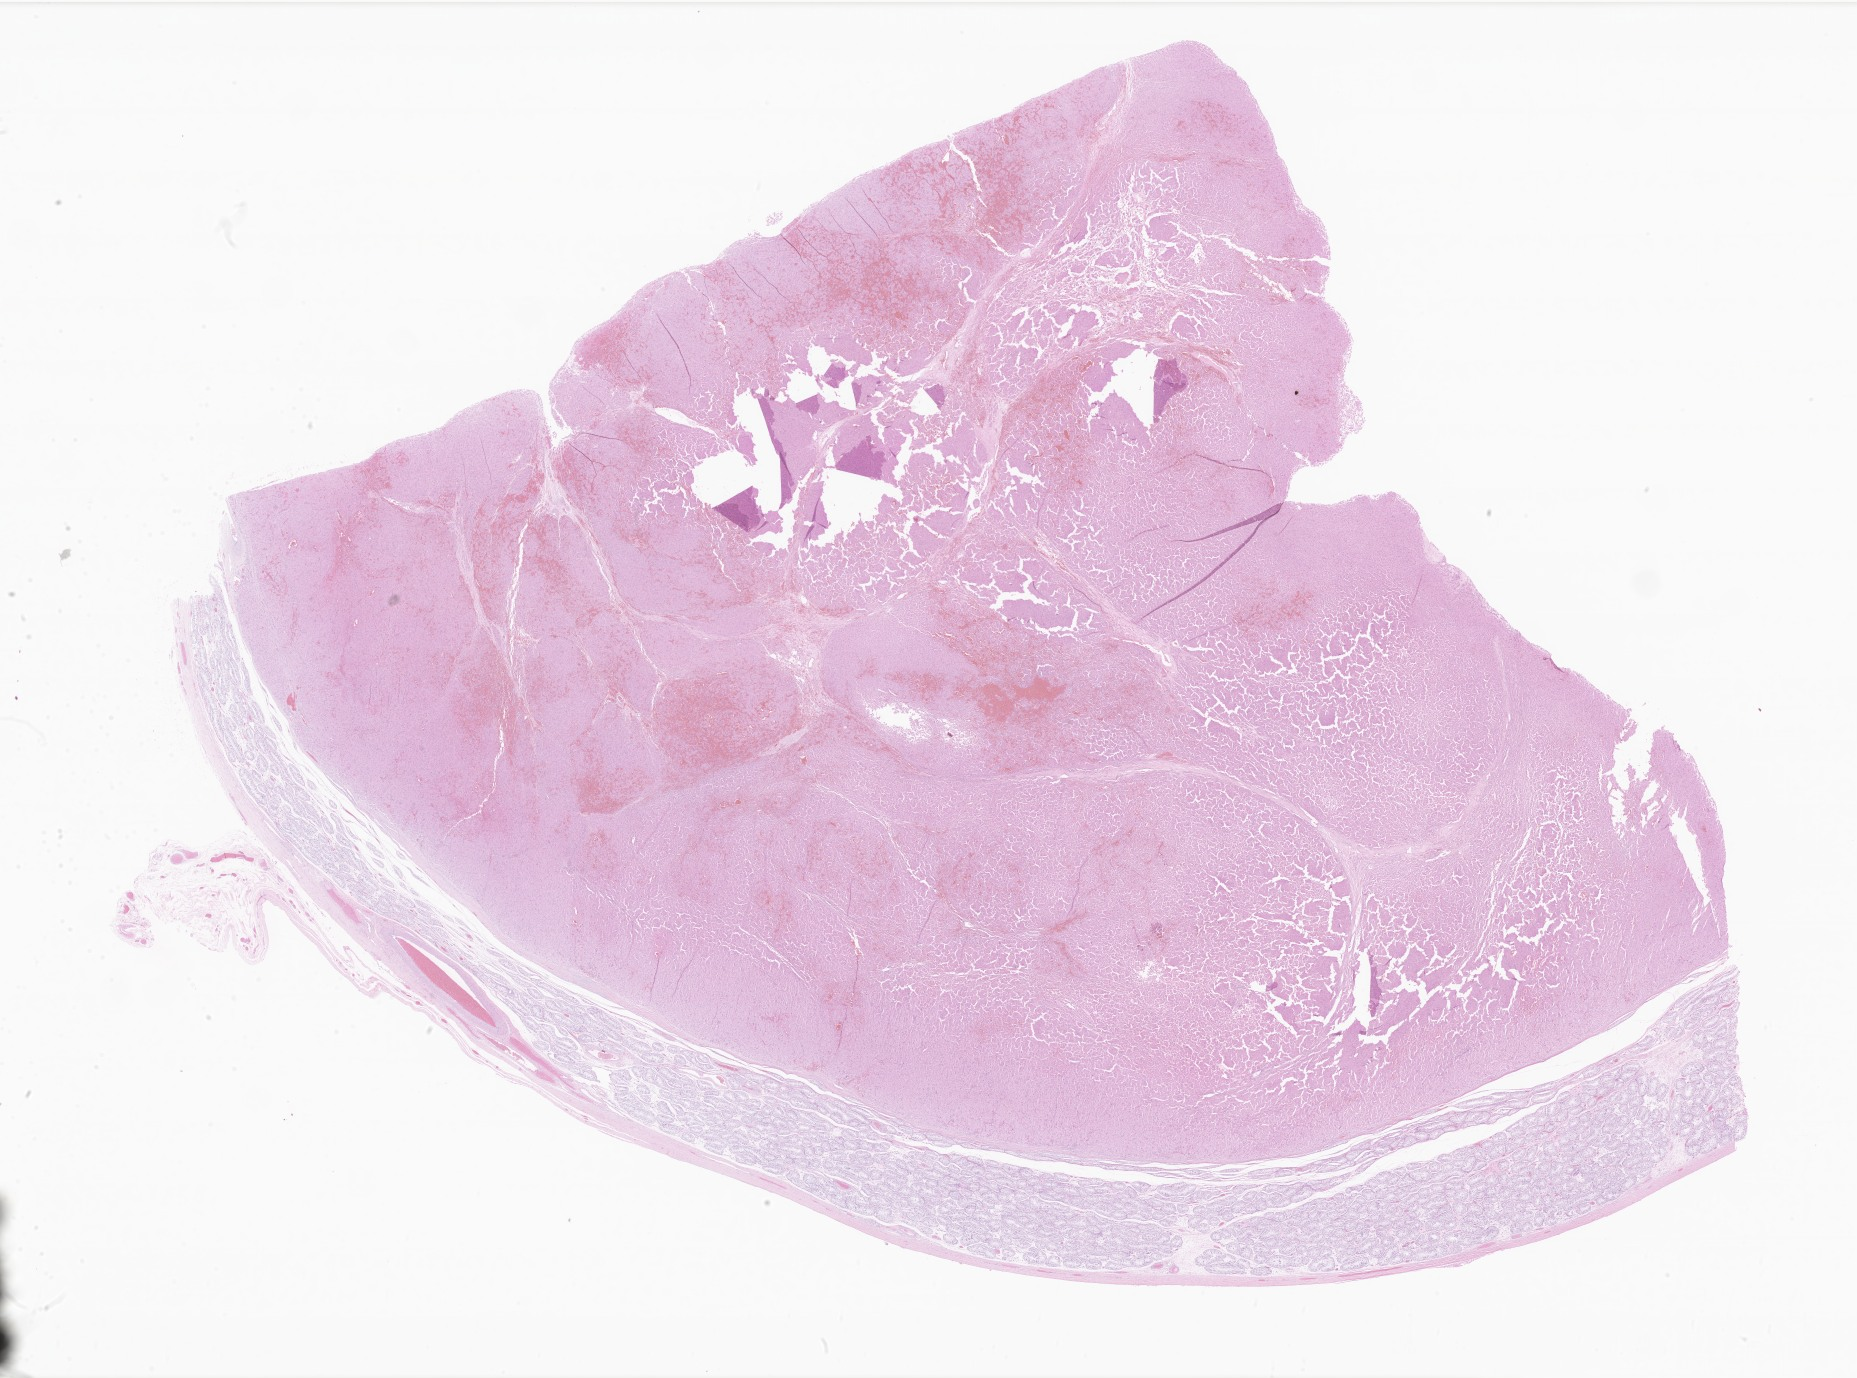
Whole-slide image, H&E stain of tumor tissue from the testis — shown as a low-resolution overview of the whole scanned area (about 31.3 x 23.2 mm). Formalin-fixed, paraffin-embedded (FFPE) tissue. Patient: male, age 208 months (17 years 4 months).
Recorded diagnosis: Leydig cell tumor of testis, NOS.